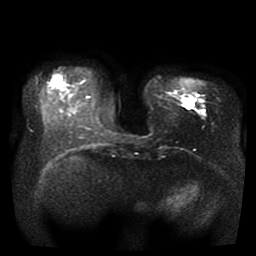
Breast MRI, one axial slice. Slice 9 of 41 in the series (ordered by position). Diffusion-weighted series; image 2 of 4 stored at this slice position (different b-values; order by instance number). 1.5 T. 5 mm slice thickness. 256 × 256 image matrix, field of view 330 × 330 mm. Female patient.
Structures marked on this image (expert manual segmentation):
- tumour on diffusion-weighted imaging: bounding box [x1, y1, x2, y2] px = [187, 101, 194, 109]